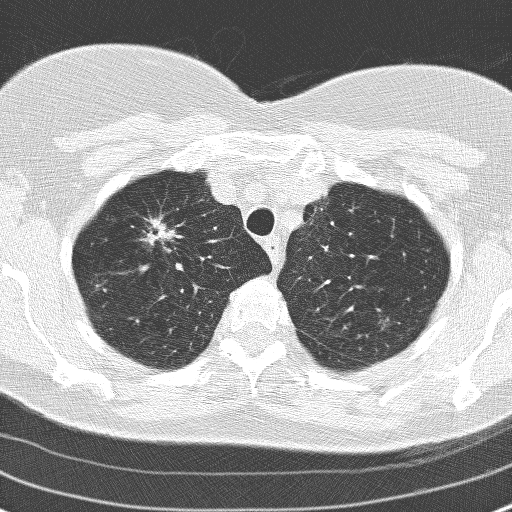
Axial slice from a low-dose chest CT screening exam, second annual screen, lung window (W 1500 / L -600 HU), 3.2 mm slice thickness, 120 kVp, slice 32 of 160 in the series, 512 × 512 image matrix, field of view 313 × 313 mm. Female participant, aged 60 years at enrolment. Former smoker at enrolment.
Expert-annotated lung lesion, box from (x=126, y=207) to (x=180, y=257) px. Screening reader's record for this exam (one nodule recorded; not confirmed to be the boxed lesion): non-calcified nodule or mass ≥4 mm, right upper lobe, 17 × 15 mm, spiculated (stellate) margins, soft tissue attenuation, pre-existing on the prior screen: yes; interval growth: yes. Later outcome: lung cancer diagnosed 78 days after this screen — adenocarcinoma, NOS, right upper lobe, moderately differentiated (G2), stage IA (AJCC 6th edition), 23 mm at pathology.